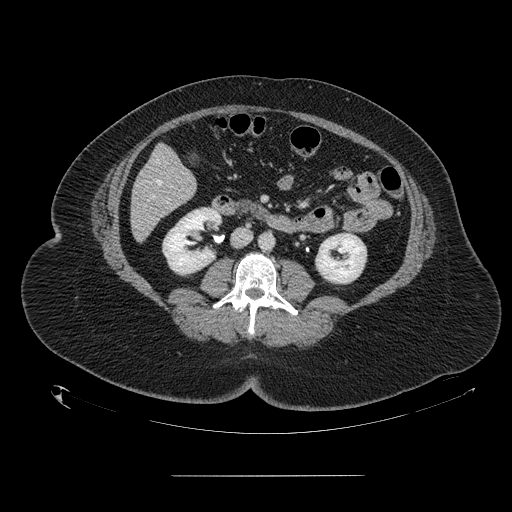
Contrast-enhanced abdominal CT, one axial slice. Slice 44 of 164 in the series (ordered by position). 120 kVp. Intravenous contrast given. Soft-tissue window (W 400 / L 40 HU). 2.5 mm slice thickness. 512 × 512 image matrix, field of view 495 × 495 mm. Female patient, age 52 years. Case-level facts recorded for this patient, not image findings: diagnosis: colorectal cancer liver metastases, imaged before liver resection; multiple liver metastases: yes; largest metastasis: 3.5 cm; disease in both lobes: no.
Annotated regions visible in this slice (outlined manually by an expert reader):
- hepatic veins: bounding box [x1, y1, x2, y2] px = [156, 161, 161, 185]
- liver: [131, 146, 196, 241]
- portal vein (with intrahepatic branches): [152, 195, 154, 197]